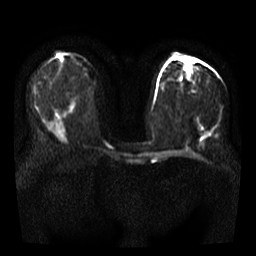
Breast MRI, one axial slice; slice 17 of 35 in the series (ordered by position); diffusion-weighted series; image 2 of 4 stored at this slice position (different b-values; order by instance number); 3 T; 256 × 256 image matrix. Female patient.
Structures marked on this image (manually delineated by an expert):
- tumour on diffusion-weighted imaging: bounding box [x1, y1, x2, y2] px = [205, 132, 208, 135]